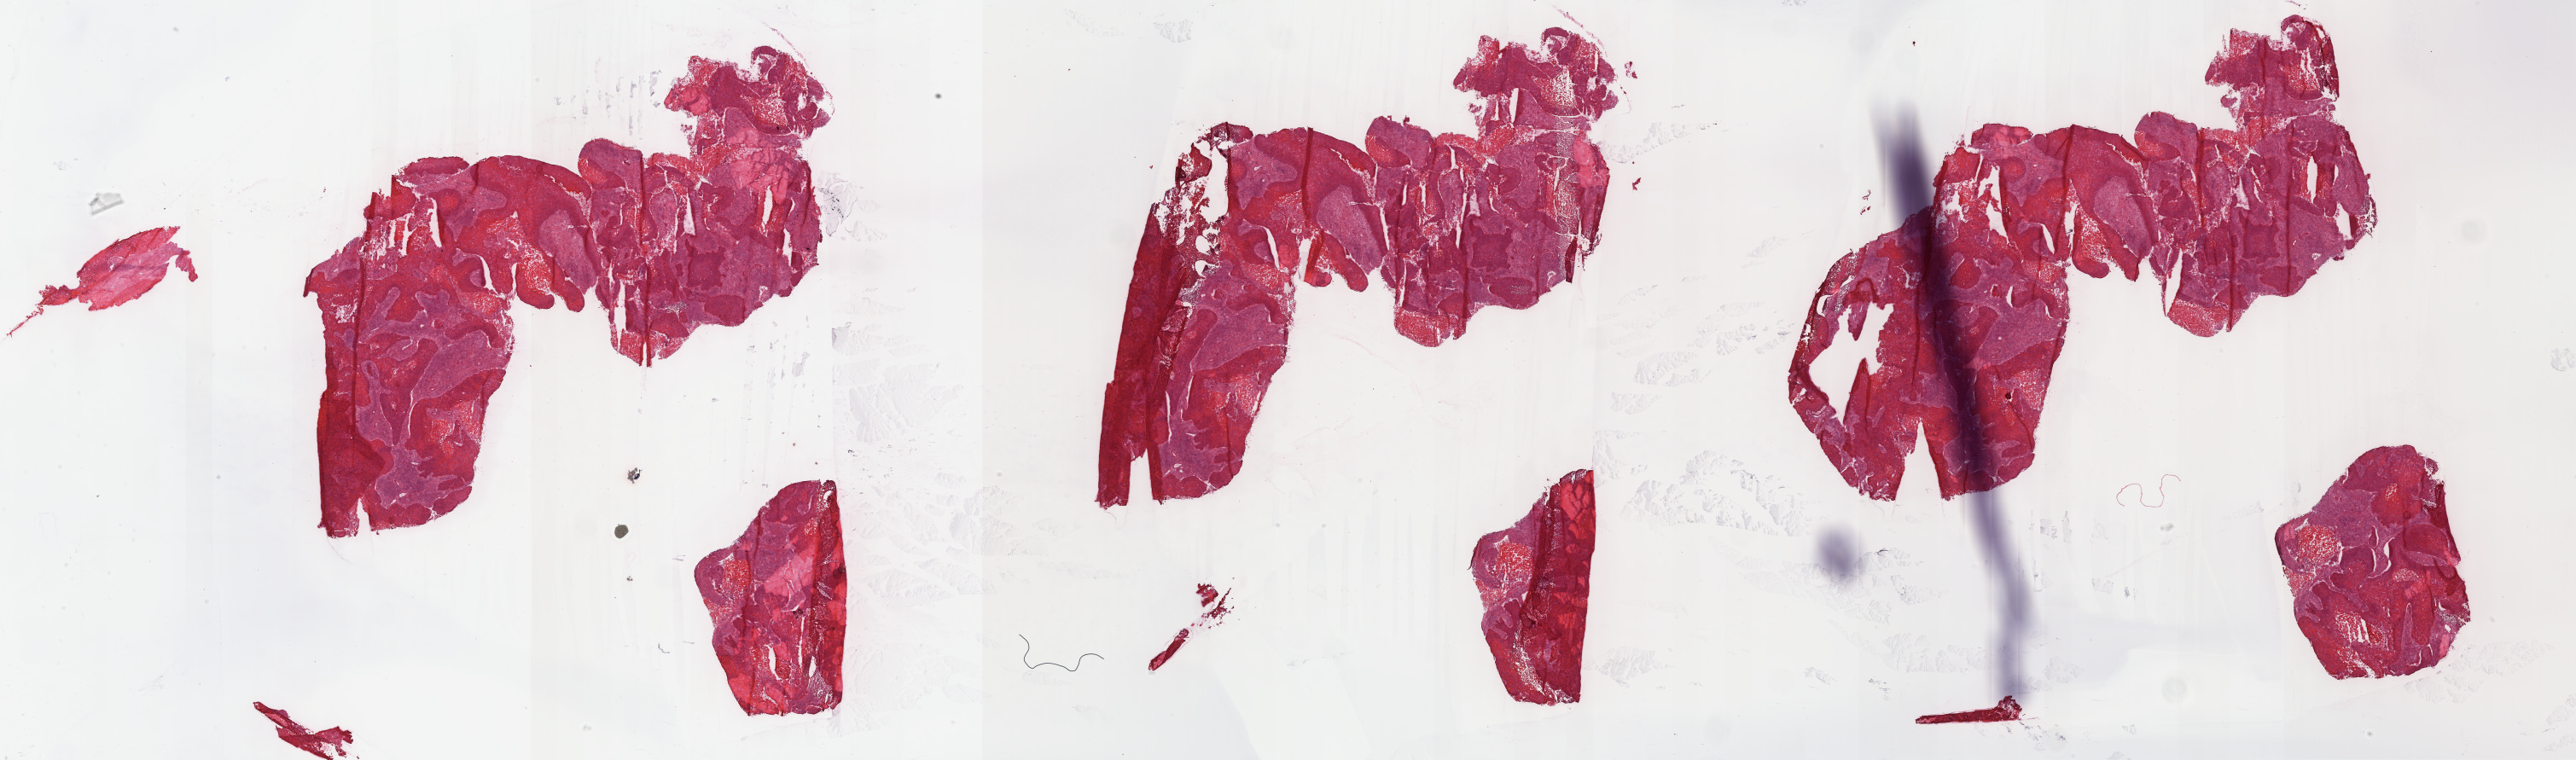
Whole-slide histology image, H&E-stained, whole scanned area (about 48.8 x 14.4 mm) shown as a low-resolution overview. Frozen section from the top of the tissue portion. Cervix, primary tumour sample. Female patient; age at initial diagnosis 44 years. Histologic grade: G2 (moderately differentiated). Pathologist review of this section (percent, as recorded): tumour cells 70%, tumour nuclei 70%, normal cells 0%, stromal cells 20%, necrosis 10%. Infiltration values recorded for this section: lymphocyte infiltration 40%, monocyte infiltration 20%, neutrophil infiltration 20%.
Diagnosis: Squamous cell carcinoma, keratinizing, NOS (cervix uteri).